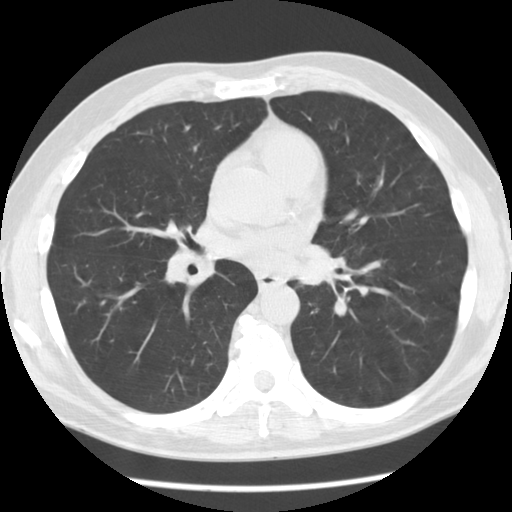
Chest CT (low-dose screening protocol), one axial image. Baseline screening round. Lung window (W 1500 / L -600 HU). 2.5 mm slice thickness. Standard (soft-tissue) reconstruction kernel (STANDARD). 120 kVp. Slice 60 of 112 in the series. 512 × 512 image matrix, field of view 340 × 340 mm. Male participant, aged 55 years at enrolment. Former smoker at enrolment.
Expert reader's lesion annotation, bounding box <278,235,351,311> (left, top, right, bottom; pixels). Screening reader's record for this exam: no non-calcified nodule ≥4 mm recorded. Official screen result: negative screen, minor abnormalities not suspicious for lung cancer. Lung cancer was diagnosed 223 days after this screen: squamous cell carcinoma, NOS, left lower lobe, moderately differentiated (G2), stage IV (AJCC 6th edition), 51 mm at pathology.